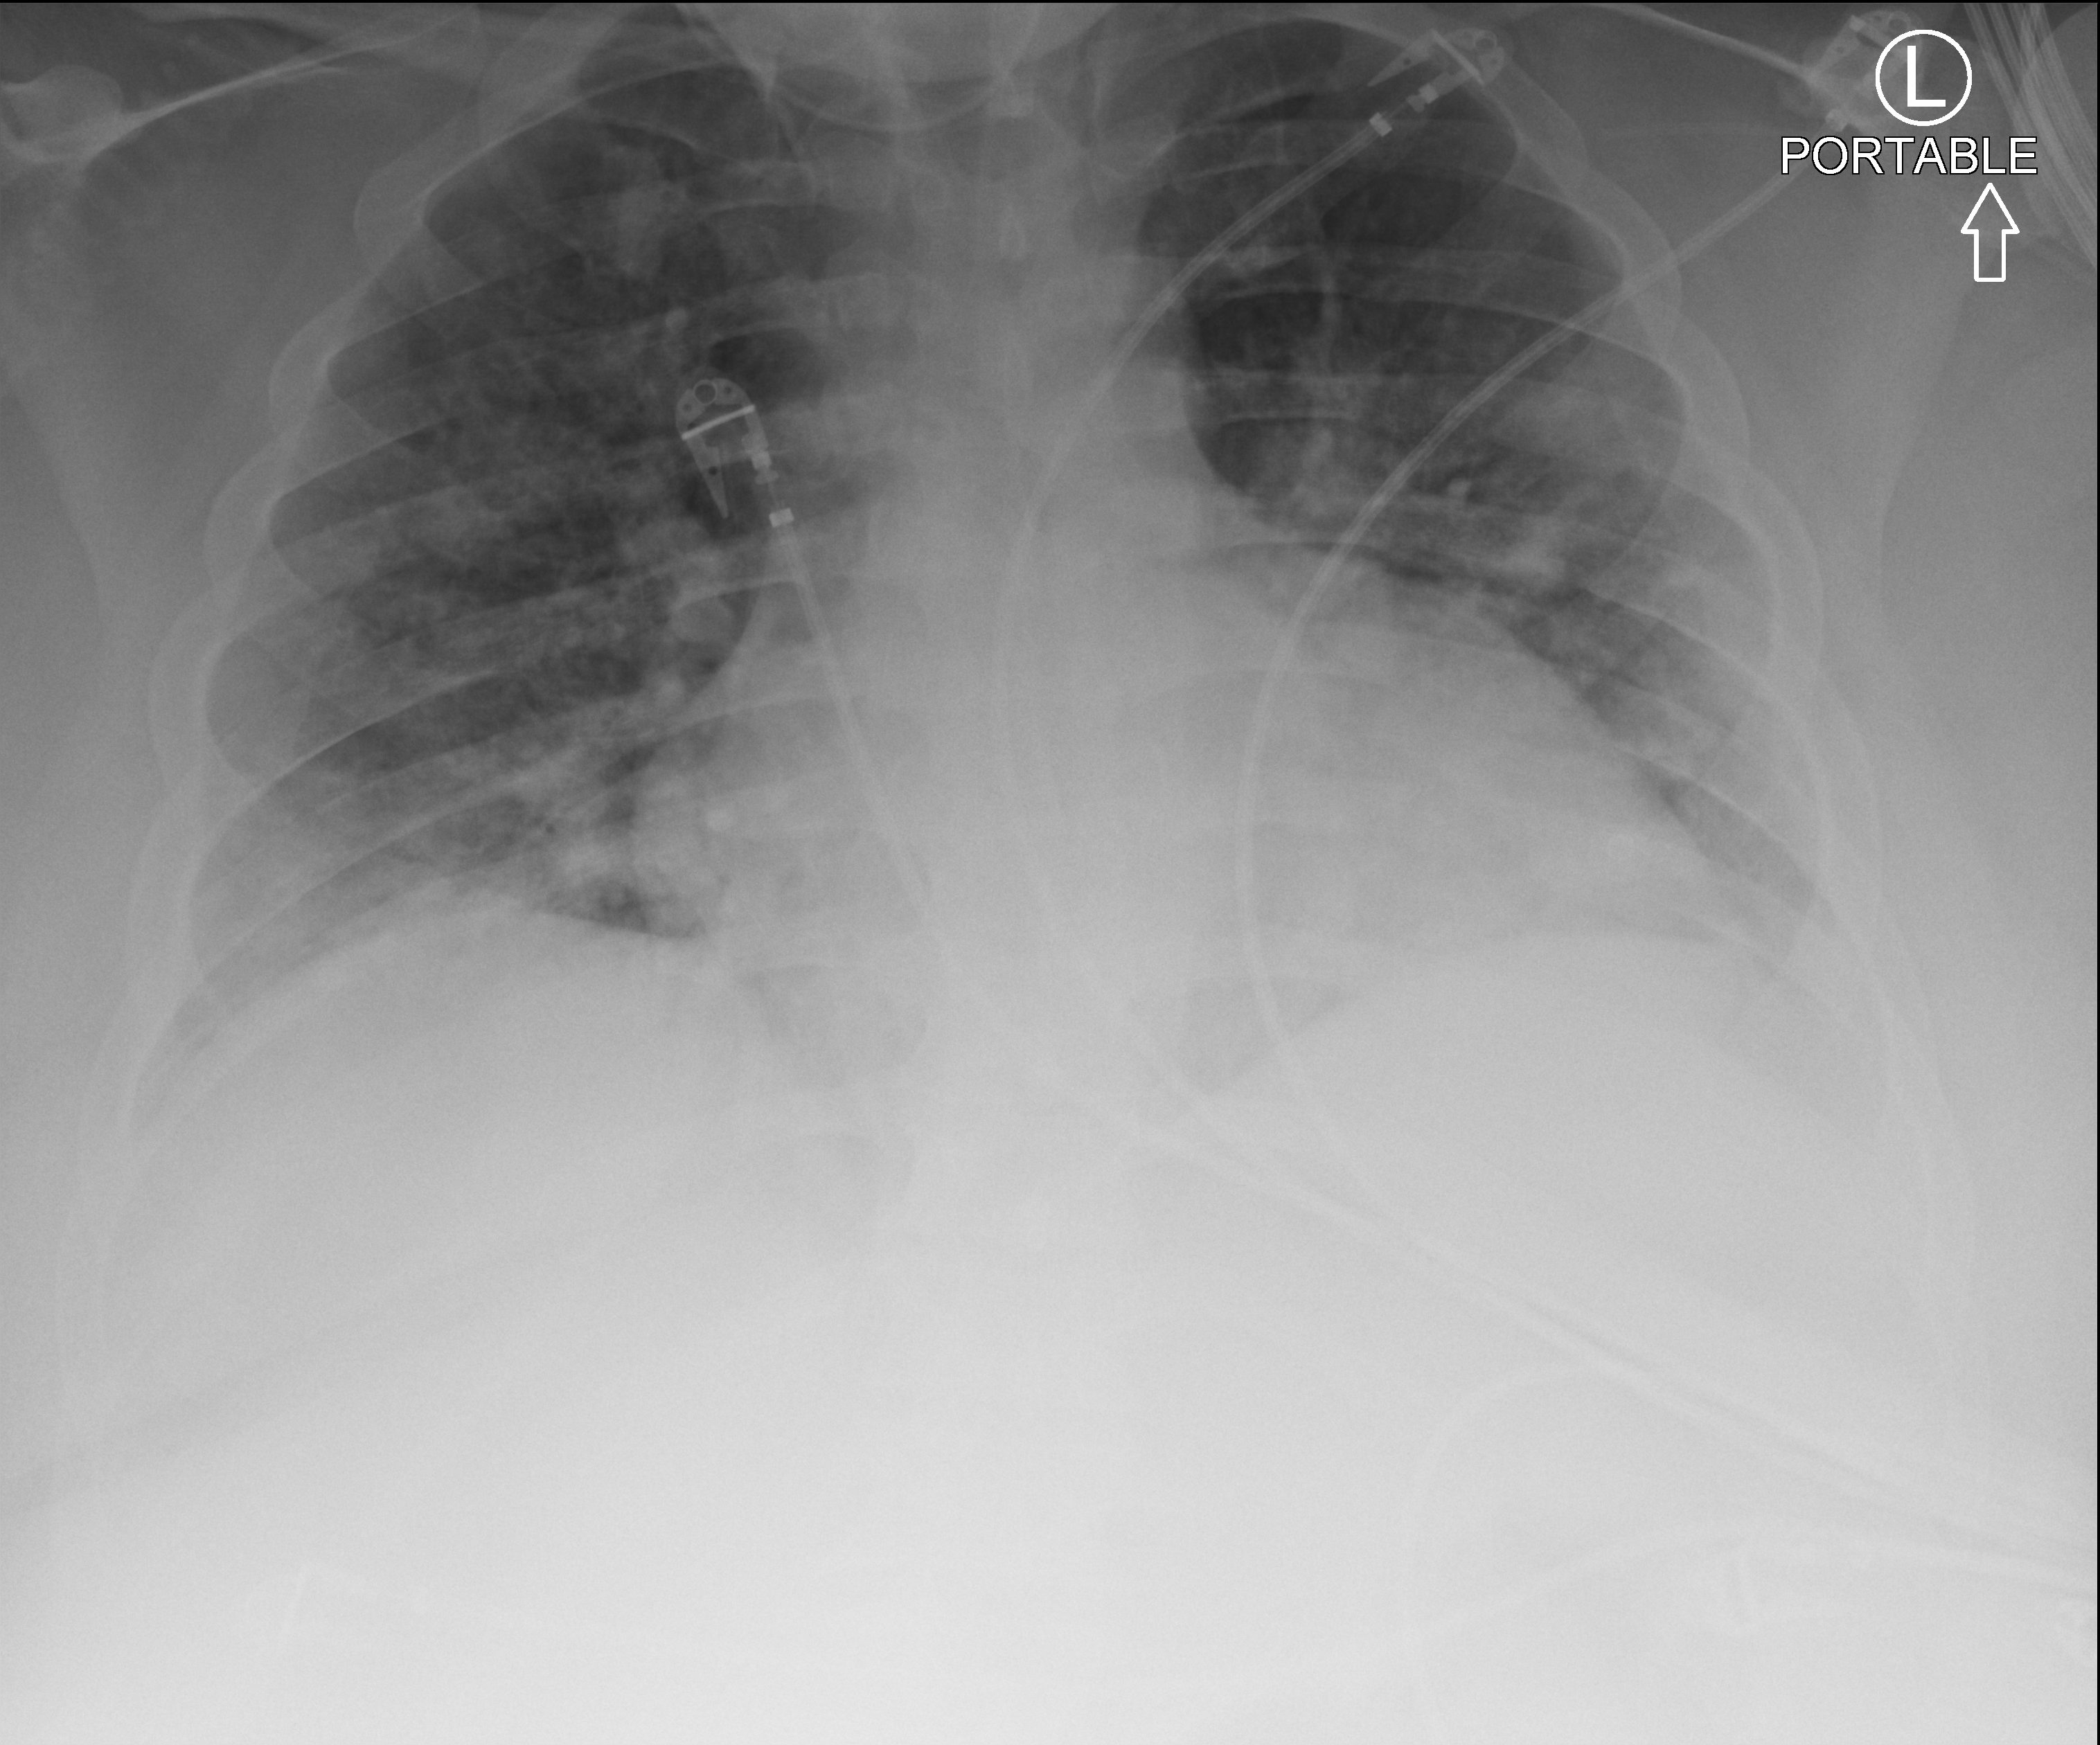
Bedside chest radiograph (computed radiography), anteroposterior (AP) projection. Male patient hospitalised with COVID-19, age 18–59 years.
From the hospital-stay record, not from the radiograph (when in the stay this image was taken is not recorded): diabetes (admission record): yes; length of hospital stay: 19 days.